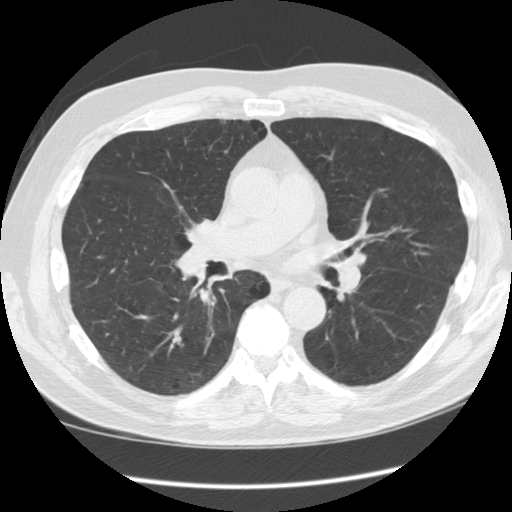
Axial slice from a low-dose chest CT screening exam, third screening round (two years after baseline), lung window (W 1500 / L -600 HU), standard (soft-tissue) reconstruction kernel (STANDARD), 120 kVp, 512 × 512 image matrix, field of view 360 × 360 mm. Male, age 60 years at enrolment.
- Expert-annotated lung lesion, bounding box <152,326,195,363> (left, top, right, bottom; pixels).
- The screening reader recorded 5 non-calcified nodules or masses ≥4 mm on this exam; which of them this box marks is not recorded.